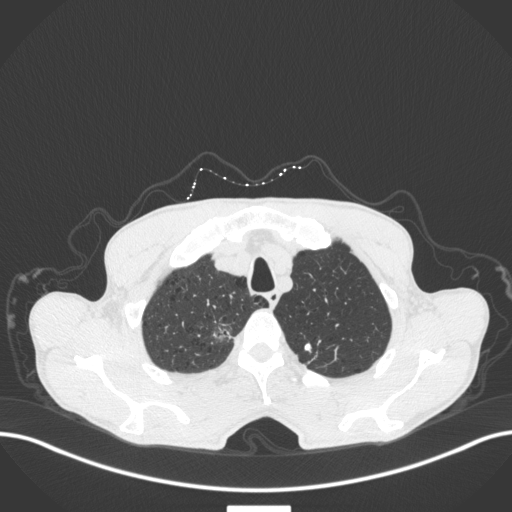
Chest CT, one axial slice. Slice 372 of 445 in the series (ordered by position). Reconstruction kernel B31f. 120 kVp. Lung window (W 1500 / L -600 HU). 1 mm slice thickness. 512 × 512 image matrix, field of view 400 × 400 mm. Male patient, age 70 years. Case-level facts recorded for this patient, not image findings: clinical TNM (as recorded): T1a N0 M0; histopathological grade: G1-2.
Outlined on this slice (bounding box drawn by a radiologist):
- lung tumour (recorded histology: adenocarcinoma): box from (x=210, y=319) to (x=237, y=345) px